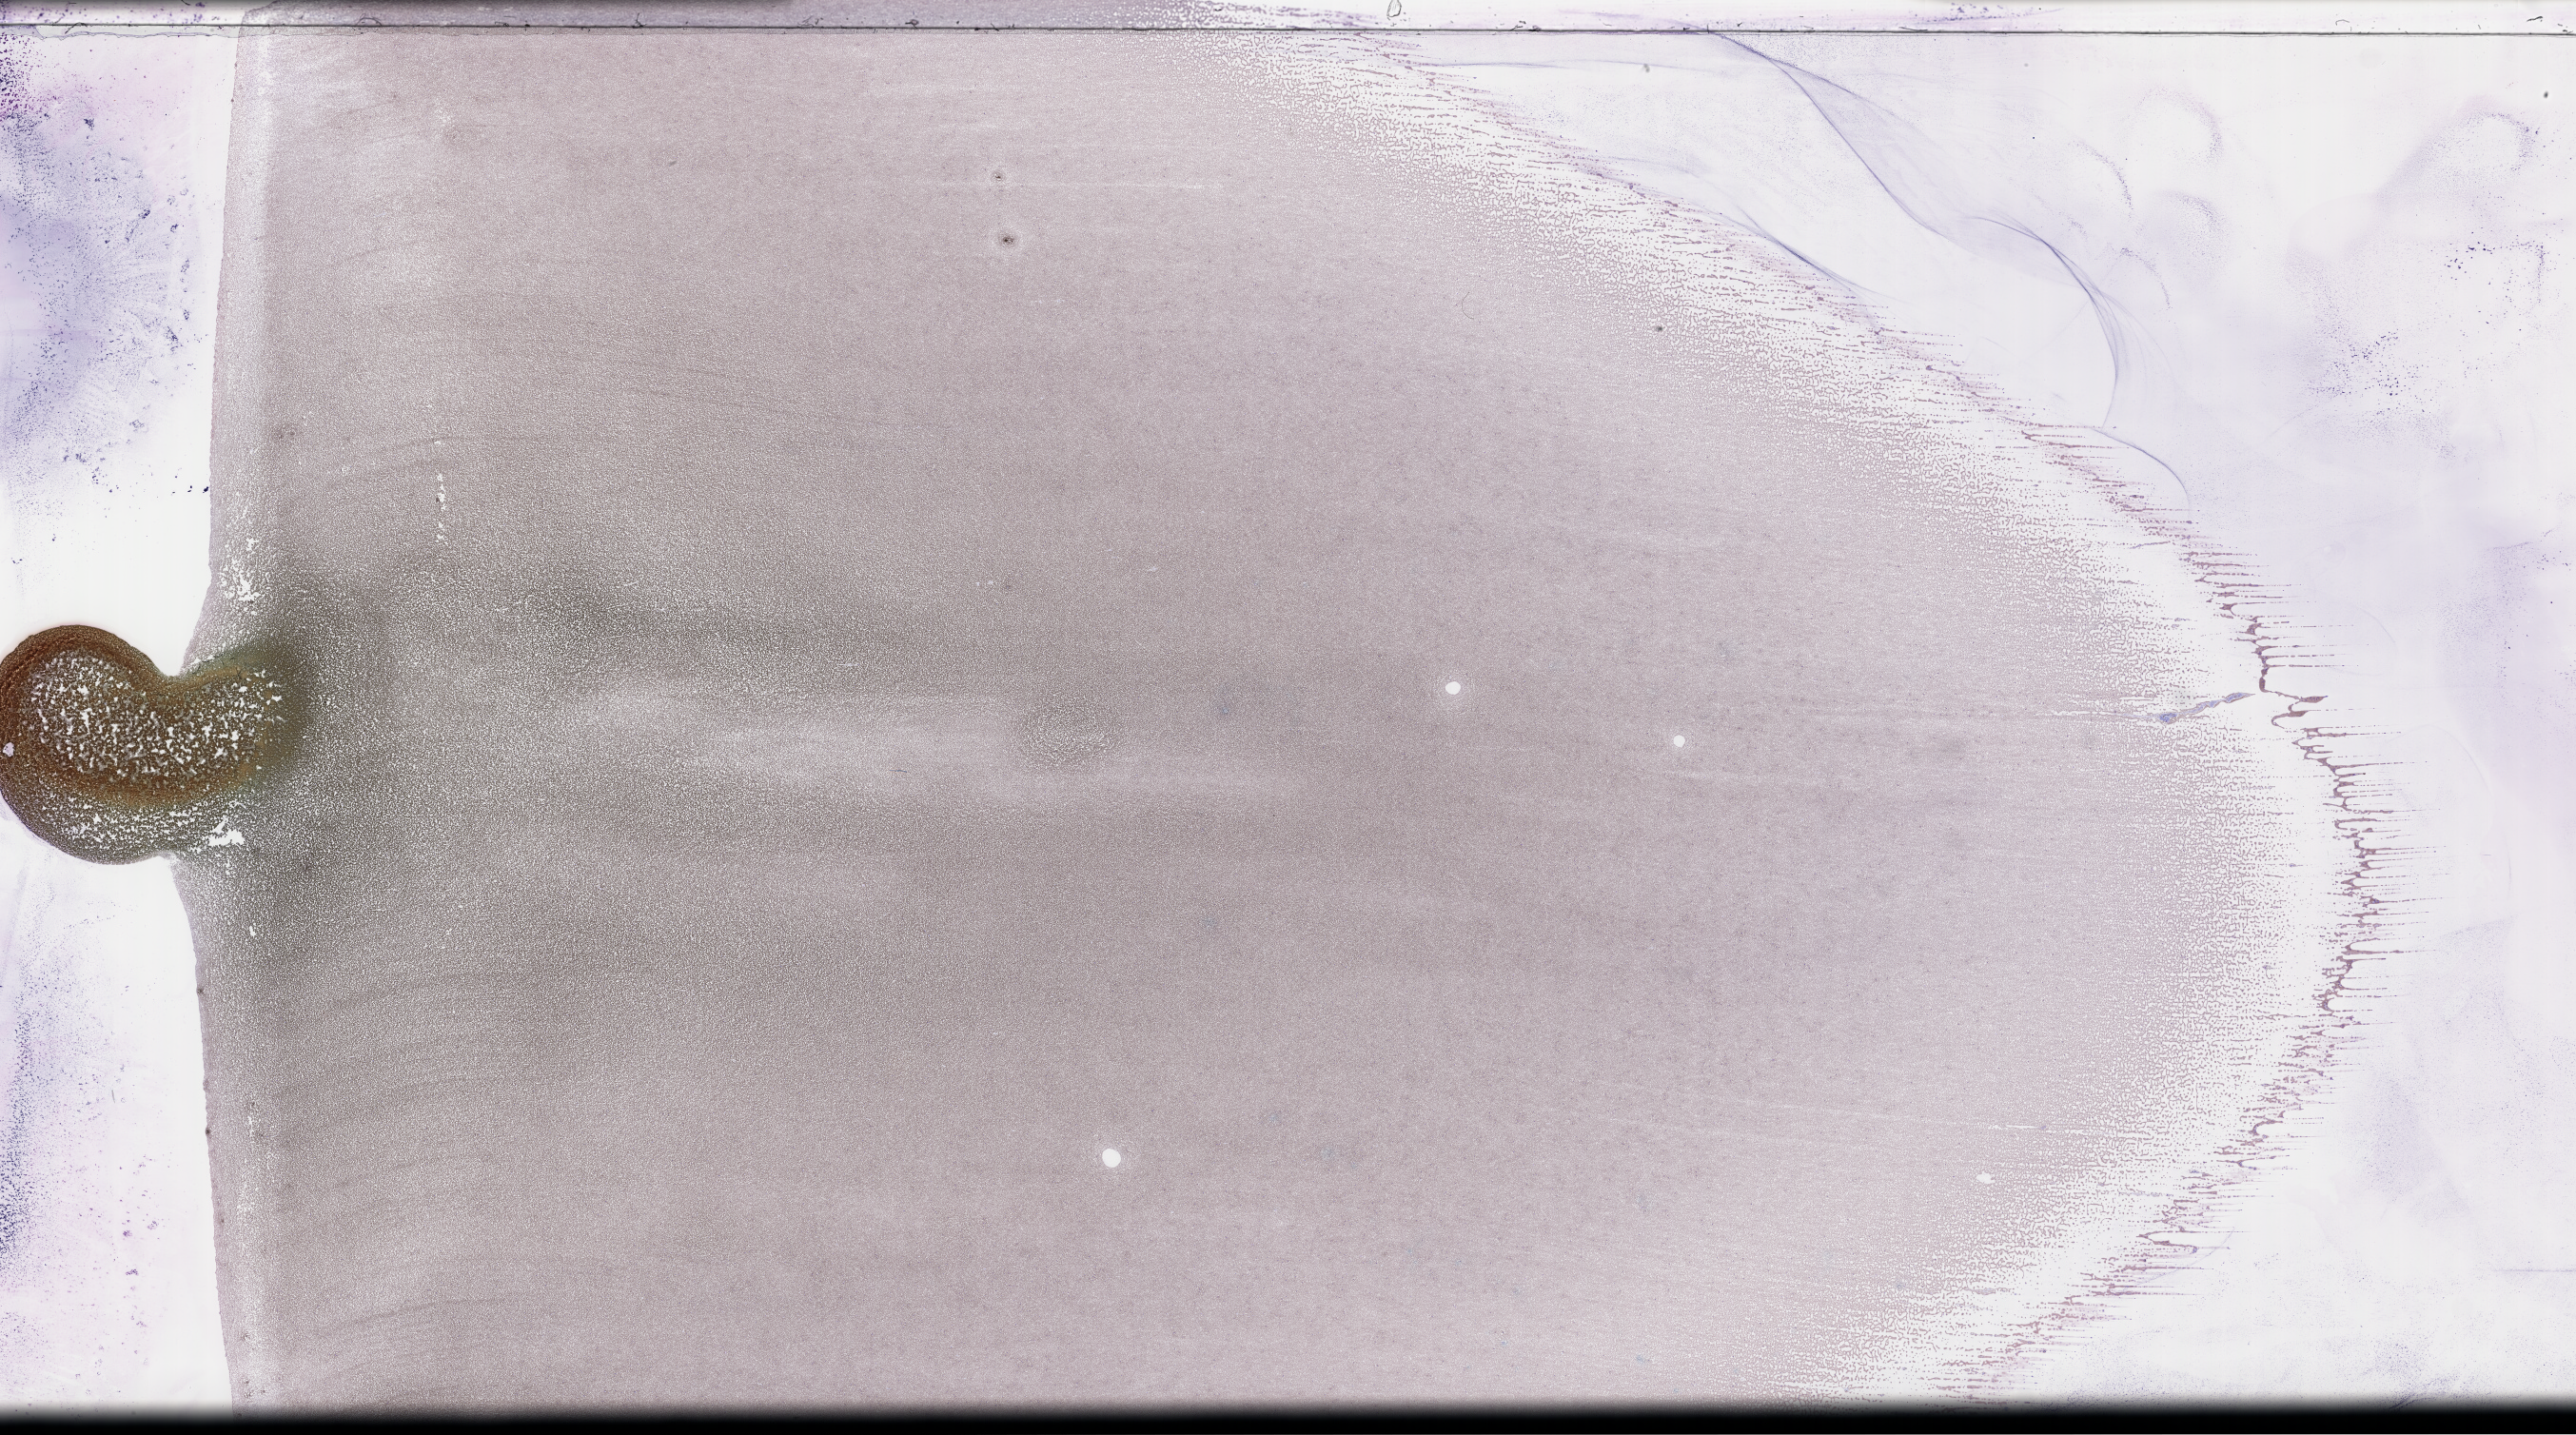
Whole-slide image of a whole blood smear, Wright-Giemsa stain — shown as a low-resolution overview of the whole scanned area (about 43.7 x 24.4 mm), EDTA-anticoagulated smear, specimen time point: collected on treatment. Patient: female.
Patient diagnosis: Plasma Cell Myeloma.